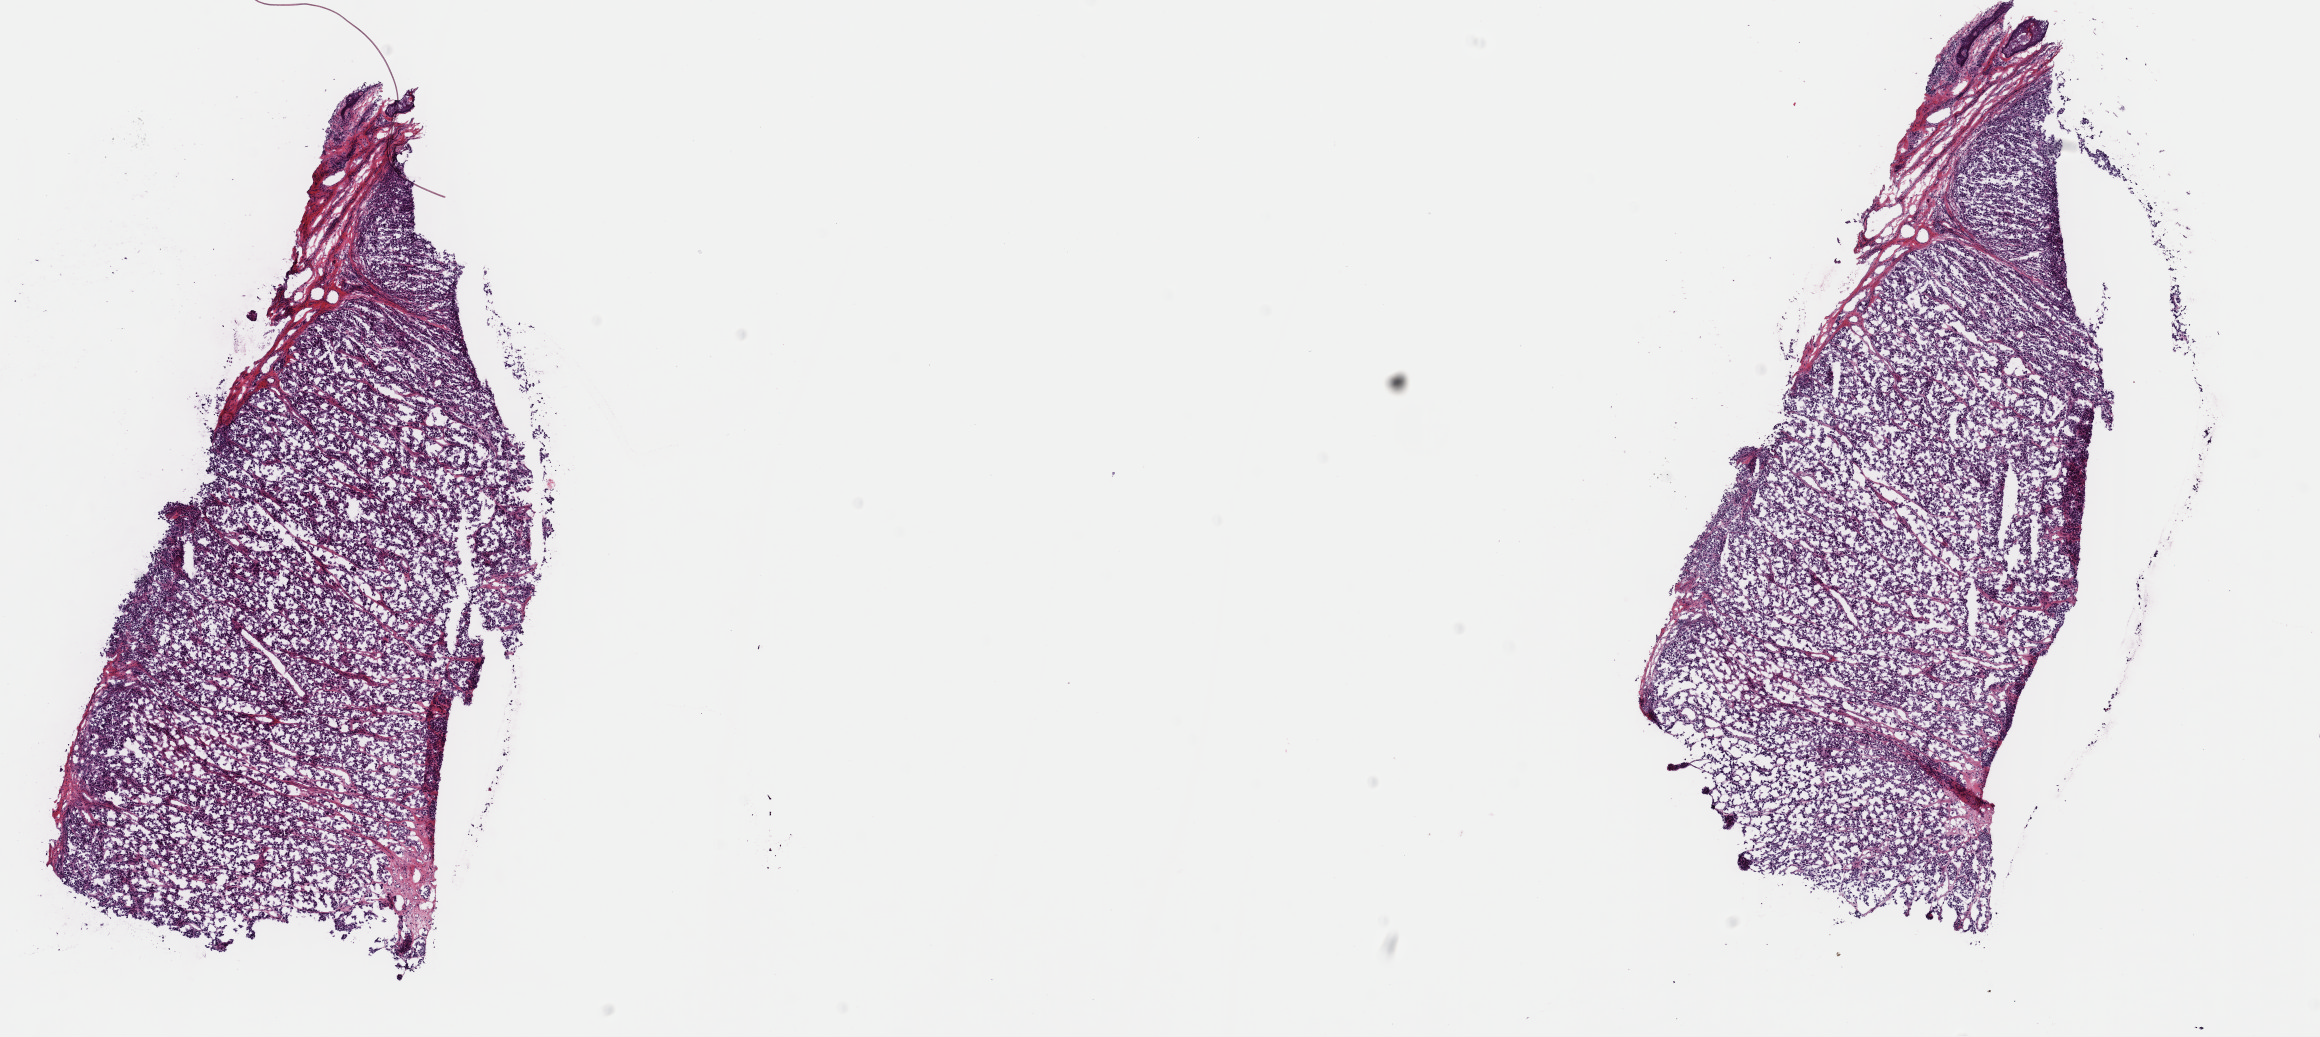
Whole-slide histology image, Hematoxylin and eosin (H&E) stained — a low-resolution overview of the entire scanned area, about 18.3 x 8.2 mm. Frozen section from the top of the tissue portion. Primary tumour sample from the skin. Male, age 69 years at initial diagnosis. Composition of this section per pathologist review: tumour cells 100%, tumour nuclei 80%, normal cells 0%, stromal cells 0%, necrosis 0%. Inflammatory infiltration, as recorded: lymphocyte infiltration 2%, monocyte infiltration 0%, neutrophil infiltration 0%.
AJCC pathologic stage: IIB (7th edition). Pathologic diagnosis: Malignant melanoma, NOS.